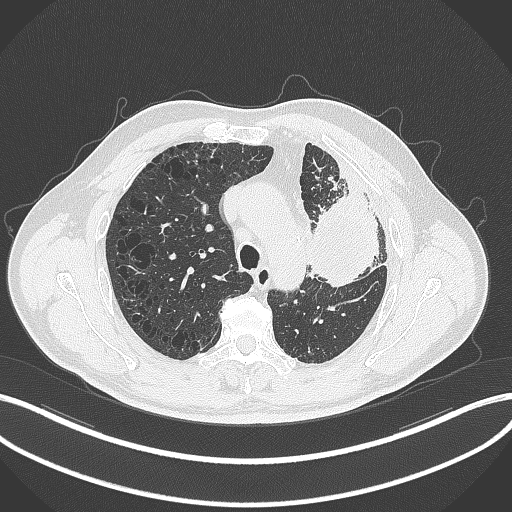
Chest CT, one axial slice; slice 226 of 297 in the series (ordered by position); reconstruction kernel B70f; 120 kVp; lung window (W 1500 / L -600 HU); 1 mm slice thickness; 512 × 512 image matrix. Patient: male, 68 years. Case-level facts recorded for this patient, not image findings: clinical TNM (as recorded): T3 N3 M1.
Outlined on this slice (bounding box drawn by a radiologist):
- lung tumour (recorded histology: adenocarcinoma): box from (x=306, y=180) to (x=385, y=290) px